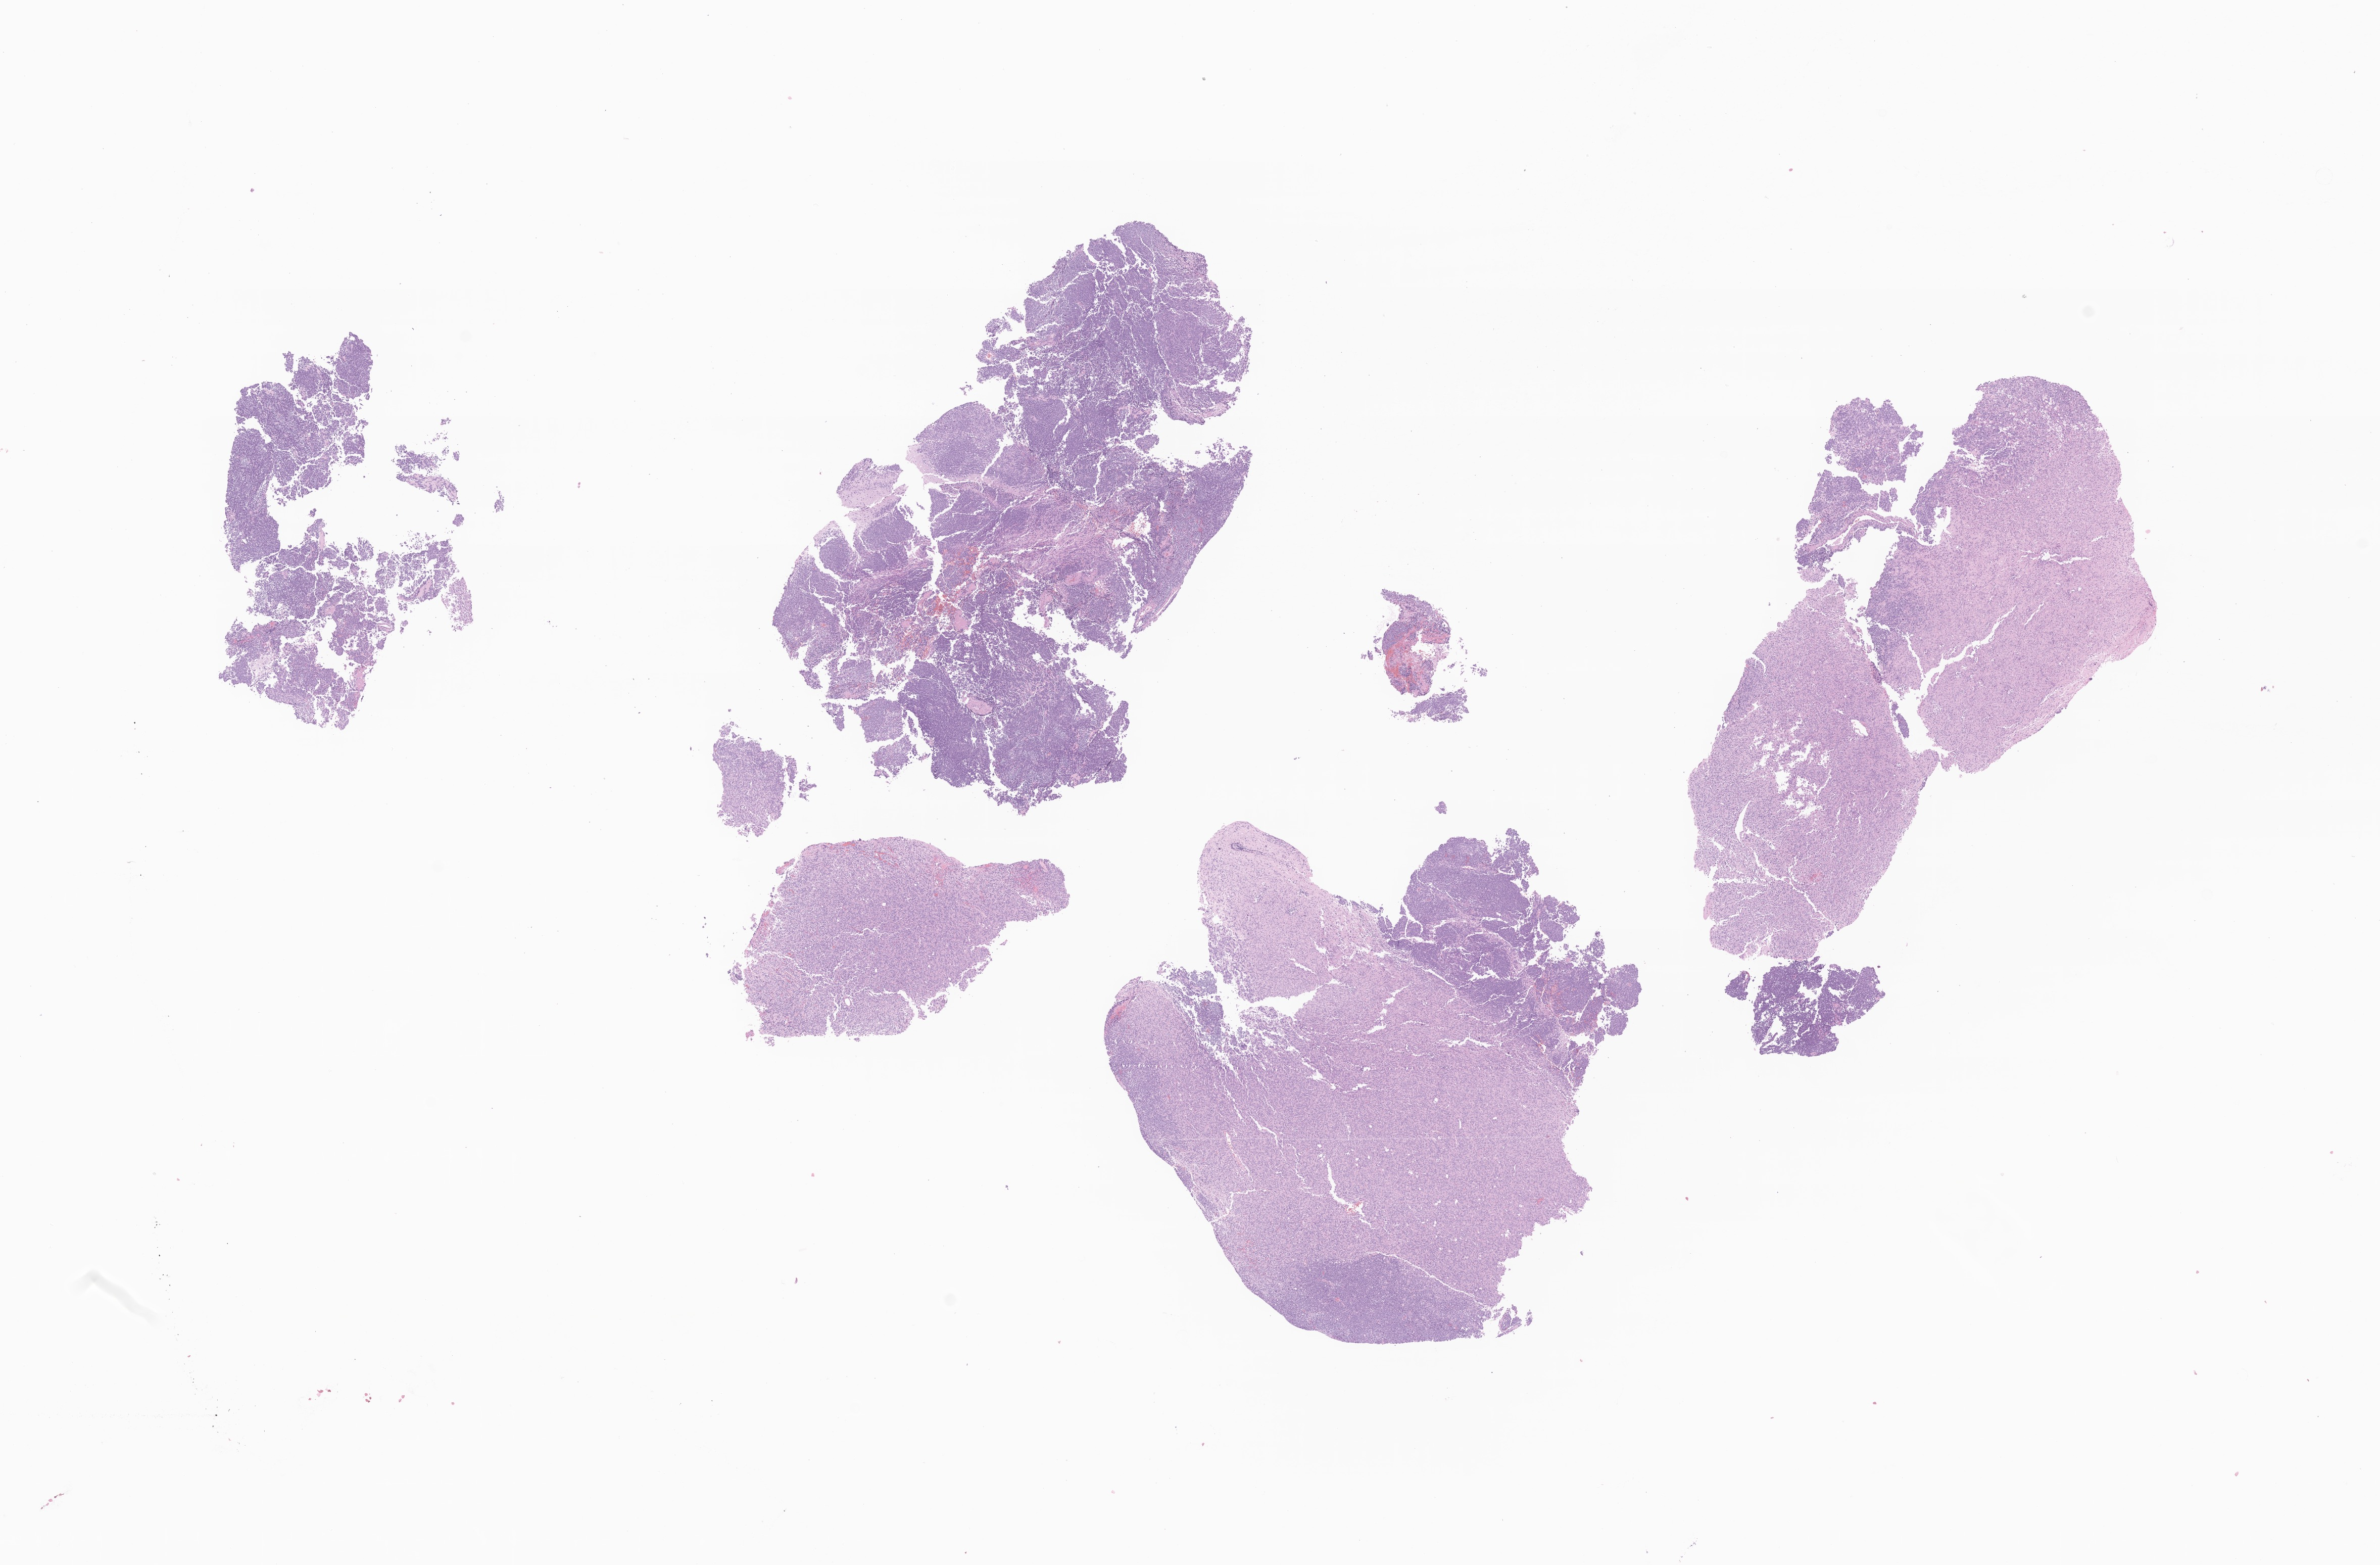
H&E whole-slide image of tumor tissue from the brain — whole scanned area (about 19.9 x 13.1 mm) shown as a low-resolution overview; formalin-fixed, paraffin-embedded (FFPE) tissue. Patient: female, age 115 months.
Diagnosis (ICD-O-3 morphology term): Medulloblastoma, NOS.